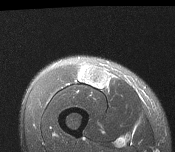
MRI of an extremity soft-tissue mass, one axial slice; slice 46 of 116 in the series (ordered by position); T2-weighted fat-saturated; MR volume resampled by the dataset authors to the PET/CT grid (not the native acquisition matrix); 3.27 mm slice thickness; 175 × 152 image matrix, field of view 171 × 148 mm. Male patient. Case-level facts recorded for this patient, not image findings: histological type: pleiomorphic leiomyosarcoma; grade: intermediate; site of the primary tumour: right thigh.
Outlined on this slice (expert contour drawn on MRI and transferred to this co-registered scan by the dataset authors):
- gross tumour volume including surrounding oedema: bounding box (x1, y1, x2, y2) in pixels: (79, 67, 110, 89)